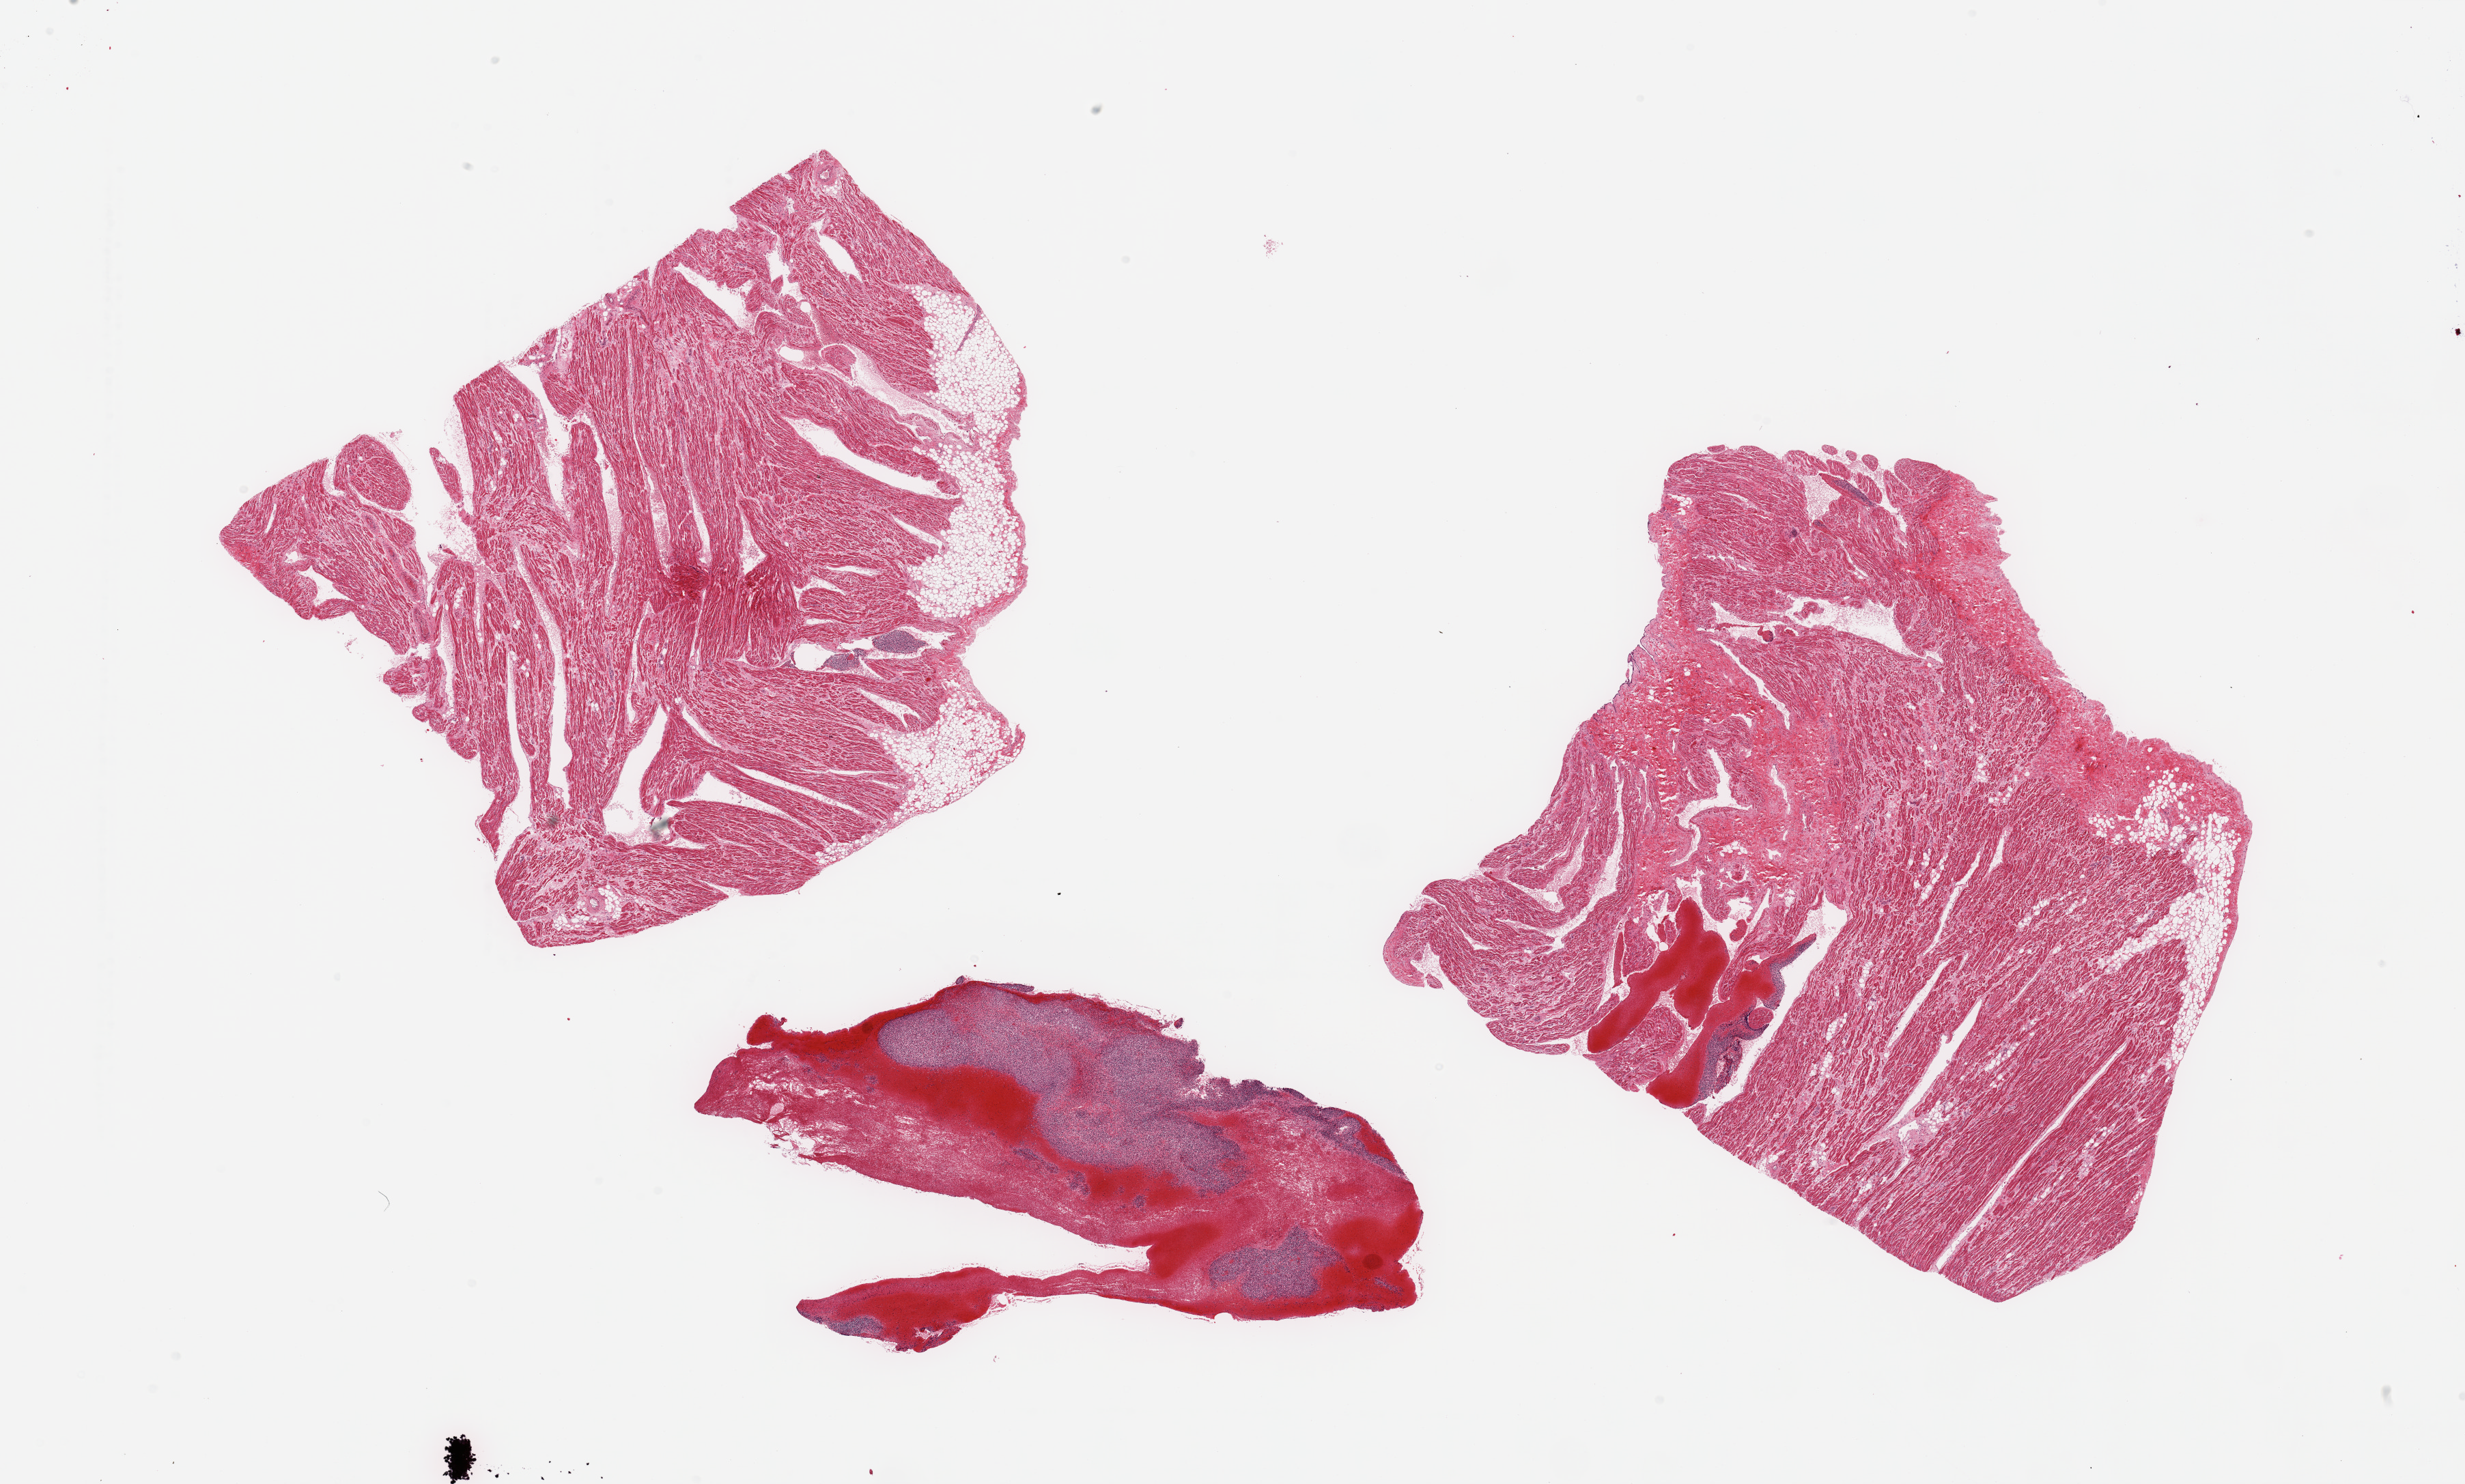
Digitized hematoxylin and eosin (H&E)-stained section, whole scanned area (about 28.5 x 17.2 mm, slide scanned at 20x) shown as a low-resolution overview, PAXgene-fixed paraffin-embedded (PFPE) section, section of auricular appendage (target tissue), tissue donor sample. Male donor.
Pathologist's review note for this sample: 3 pieces; includes 5-10% fat and attached and separate fragments of organizing blood clot.